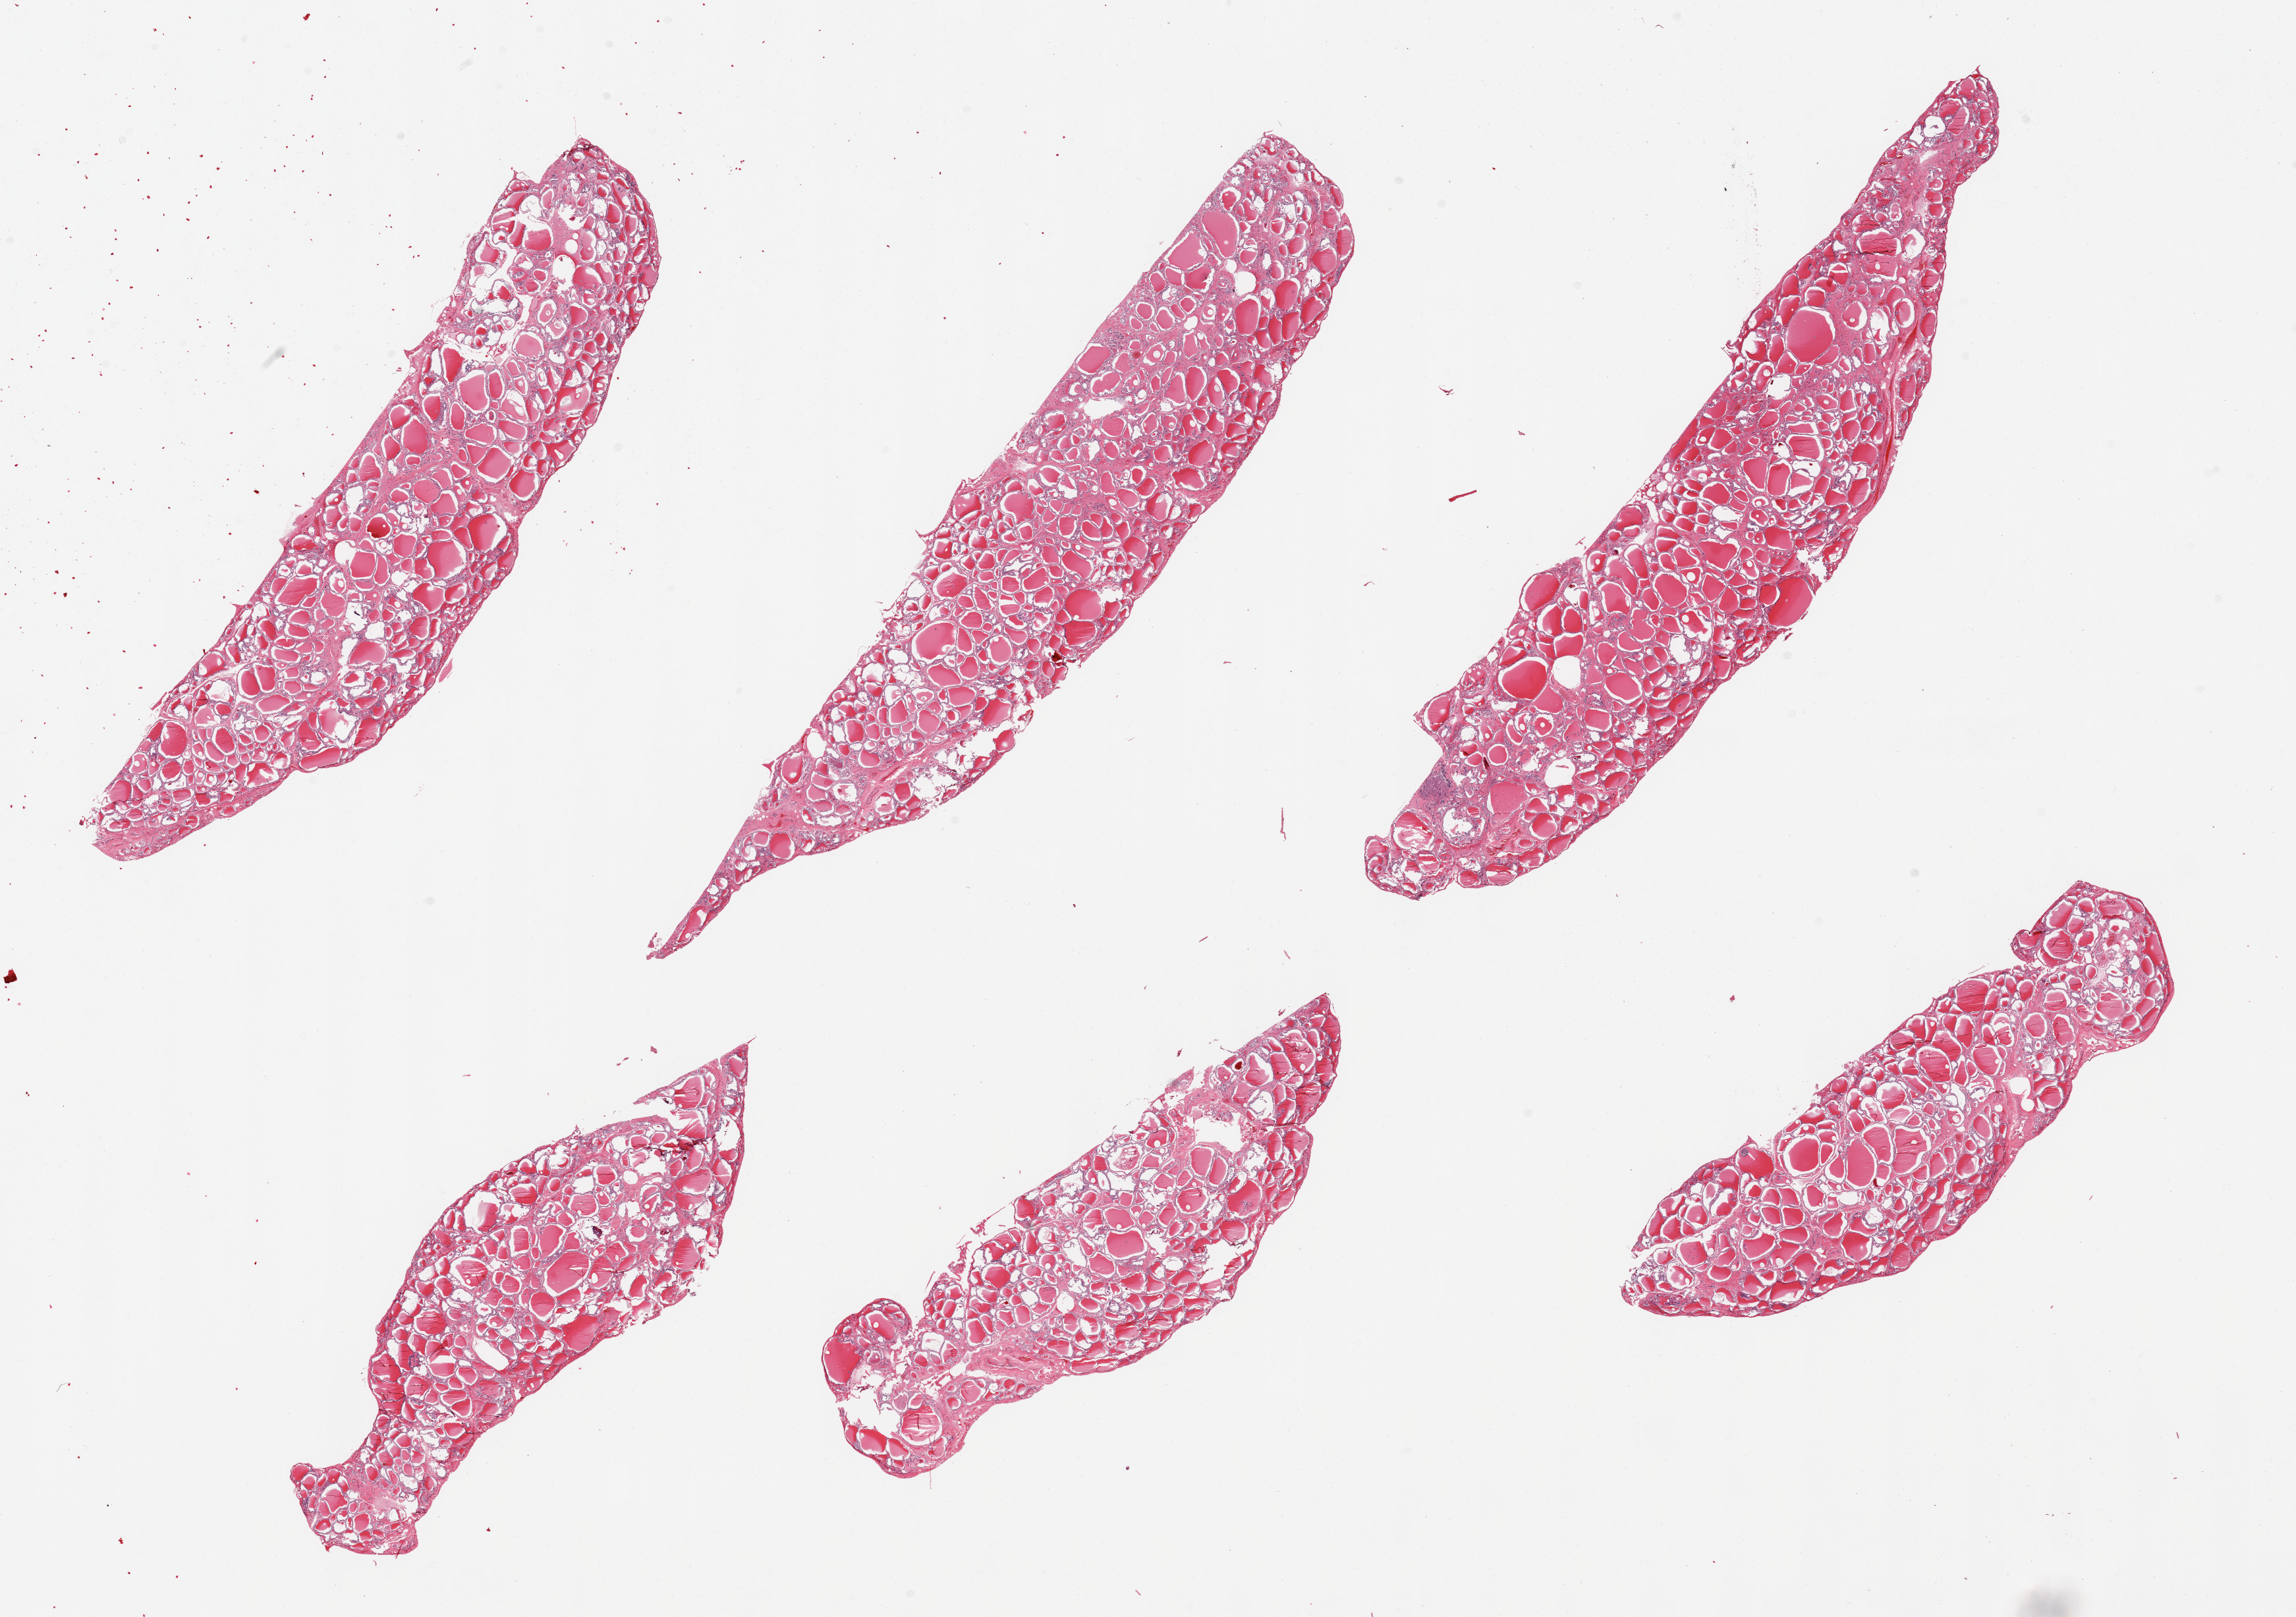
Haematoxylin and eosin whole-slide image, shown as a low-resolution overview of the whole scanned area (about 27.6 x 19.4 mm, acquisition: 20x scan). PAXgene-fixed paraffin-embedded (PFPE) section. Section of thyroid (target tissue). Tissue donor sample.
• pathologist's review note for this sample: 6 pieces, no abnormalities